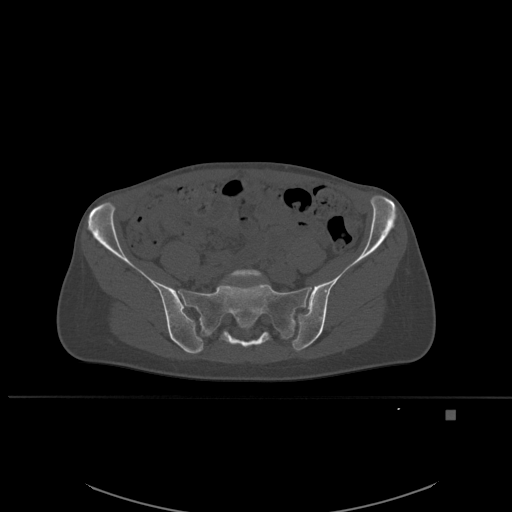
CT including the spine, one axial slice. Bone window (W 1800 / L 400 HU). 512 × 512 image matrix, field of view 440 × 440 mm. Patient: female, 45 years. Case-level facts recorded for this patient, not image findings: primary cancer: lung.
Structures marked on this image (semi-automatically segmented with operator editing):
- L5 vertebra: bounding box (x1, y1, x2, y2) in pixels: (226, 269, 264, 283)